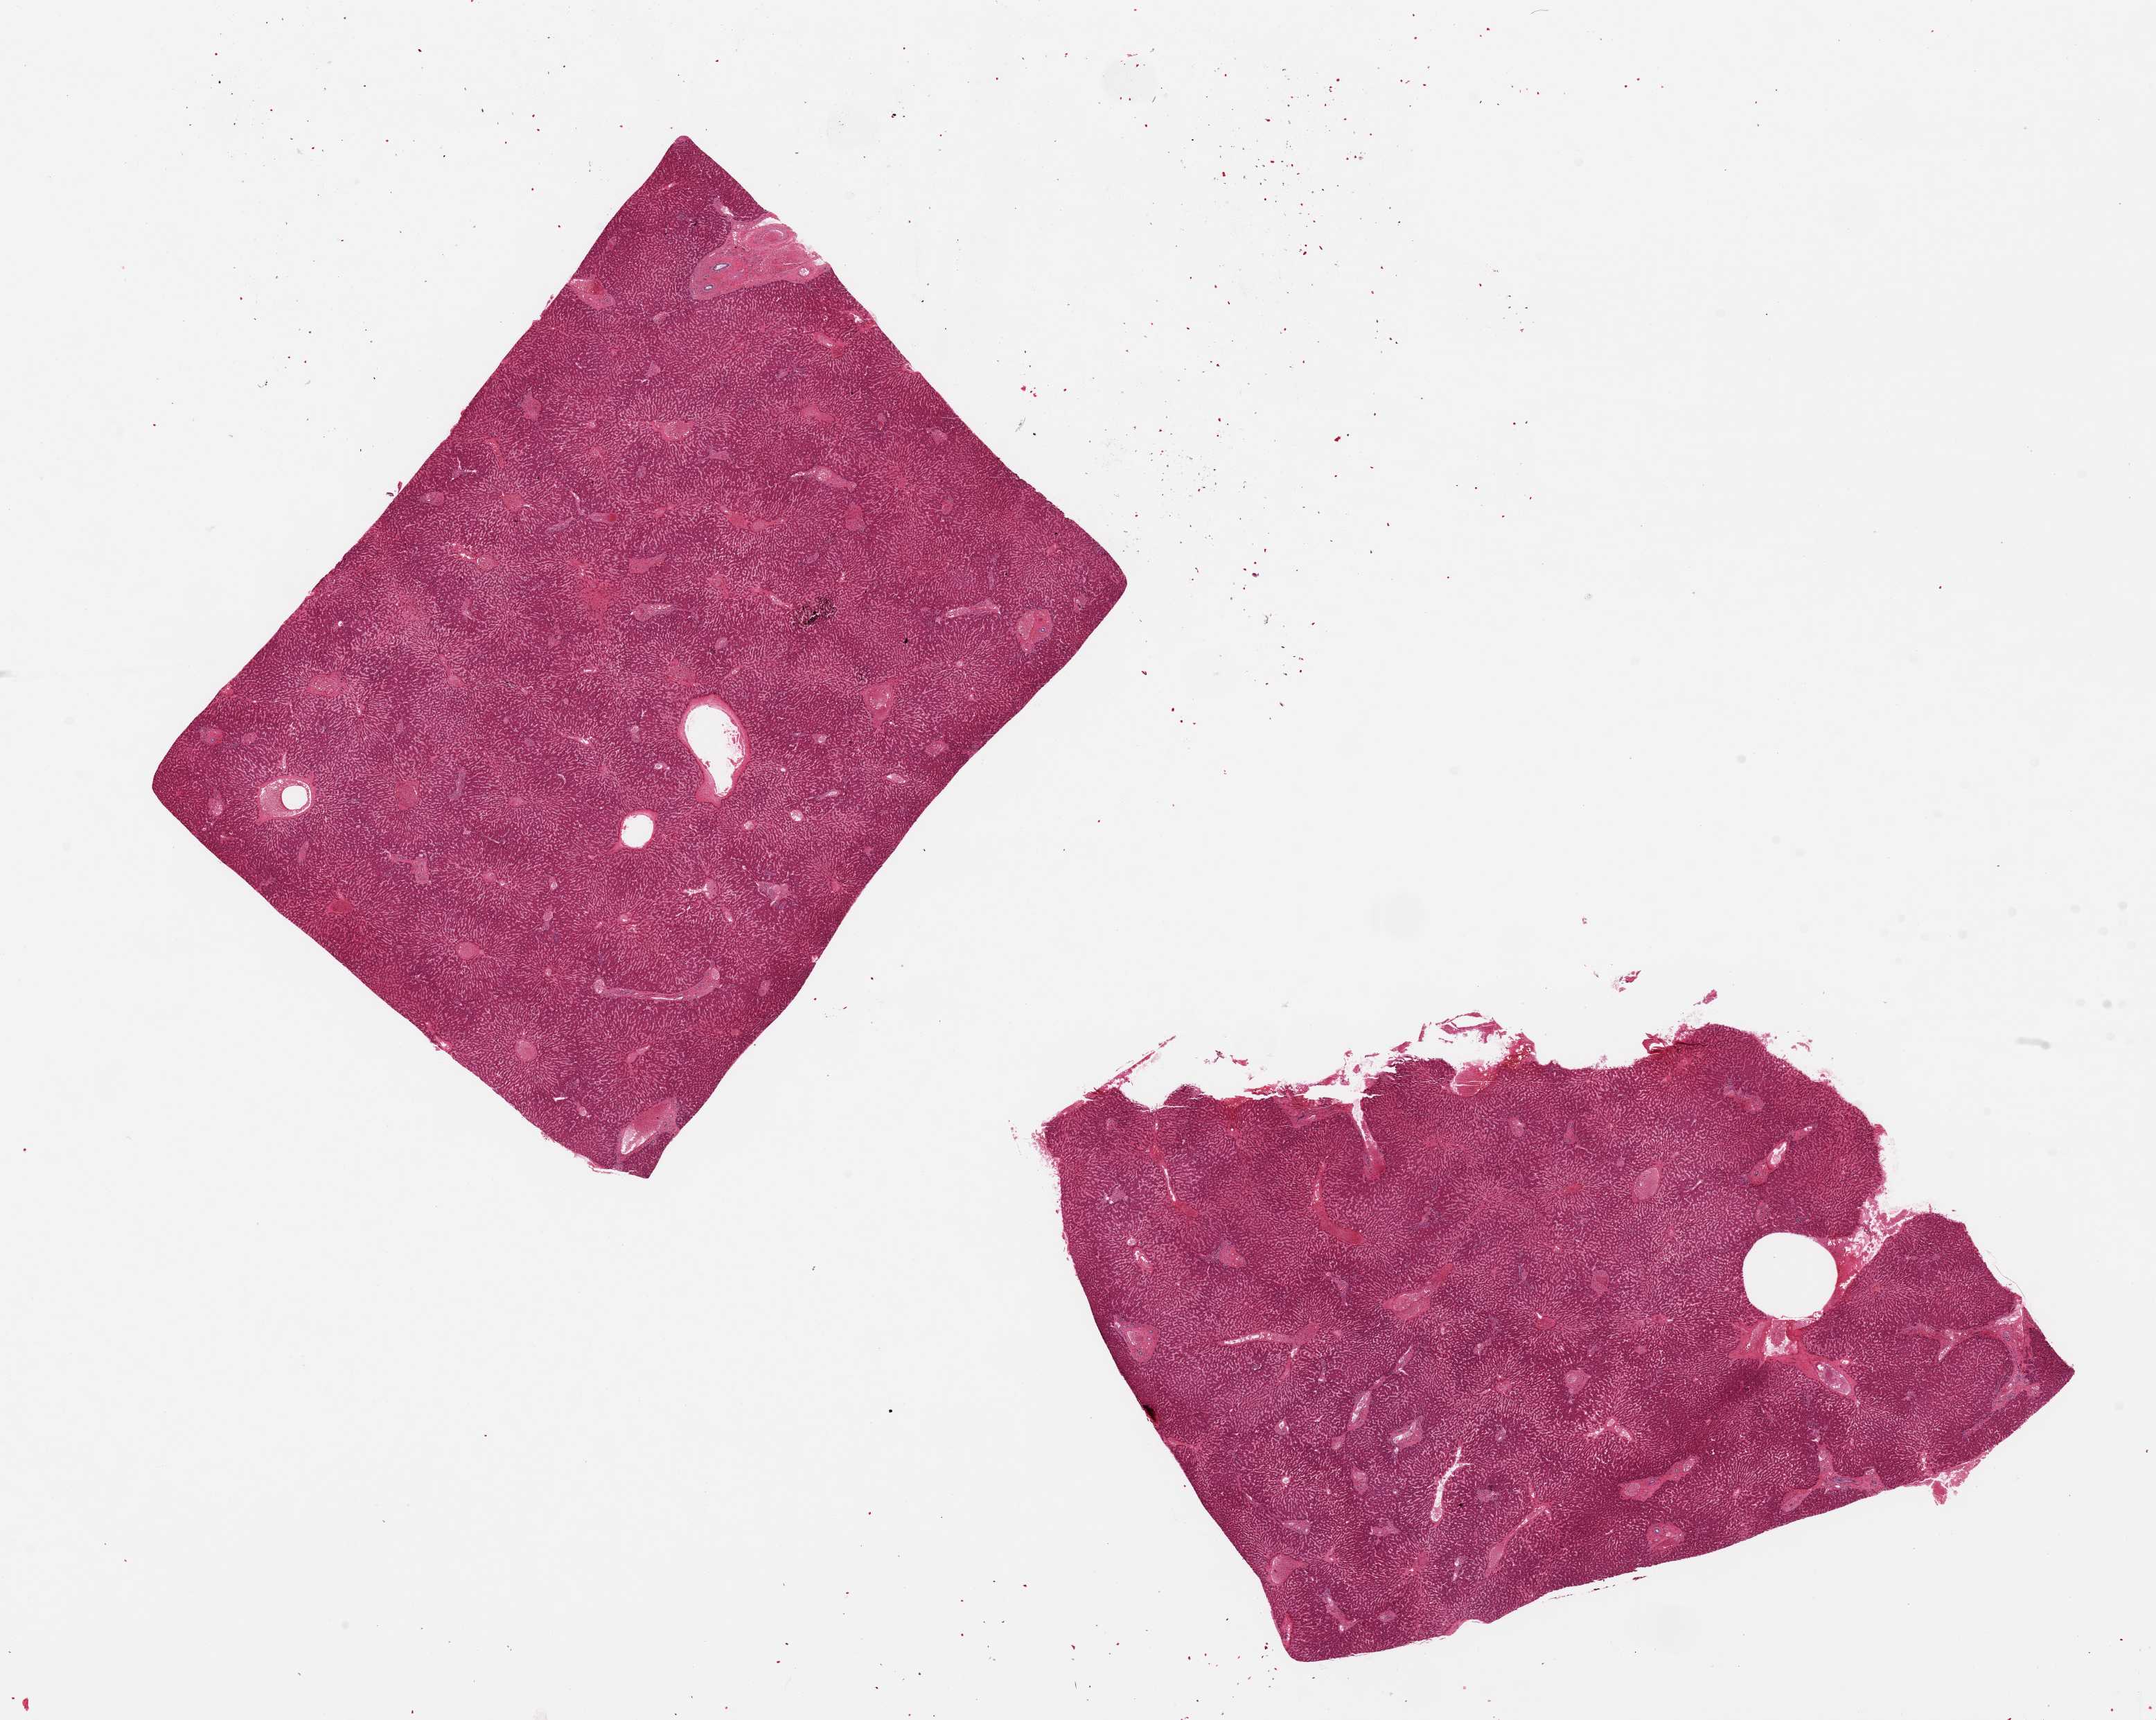
Hematoxylin and eosin (H&E) whole-slide image, low-resolution overview of the scanned area, about 24.6 x 19.6 mm (acquisition: 20x scan); PAXgene-fixed paraffin-embedded (PFPE) section; sampled site (target tissue): liver; tissue donor sample.
* reviewer comment on this tissue sample: 2 pieces, 10x7 & 9x7mm. Central vein congestion and central lobular atrophy